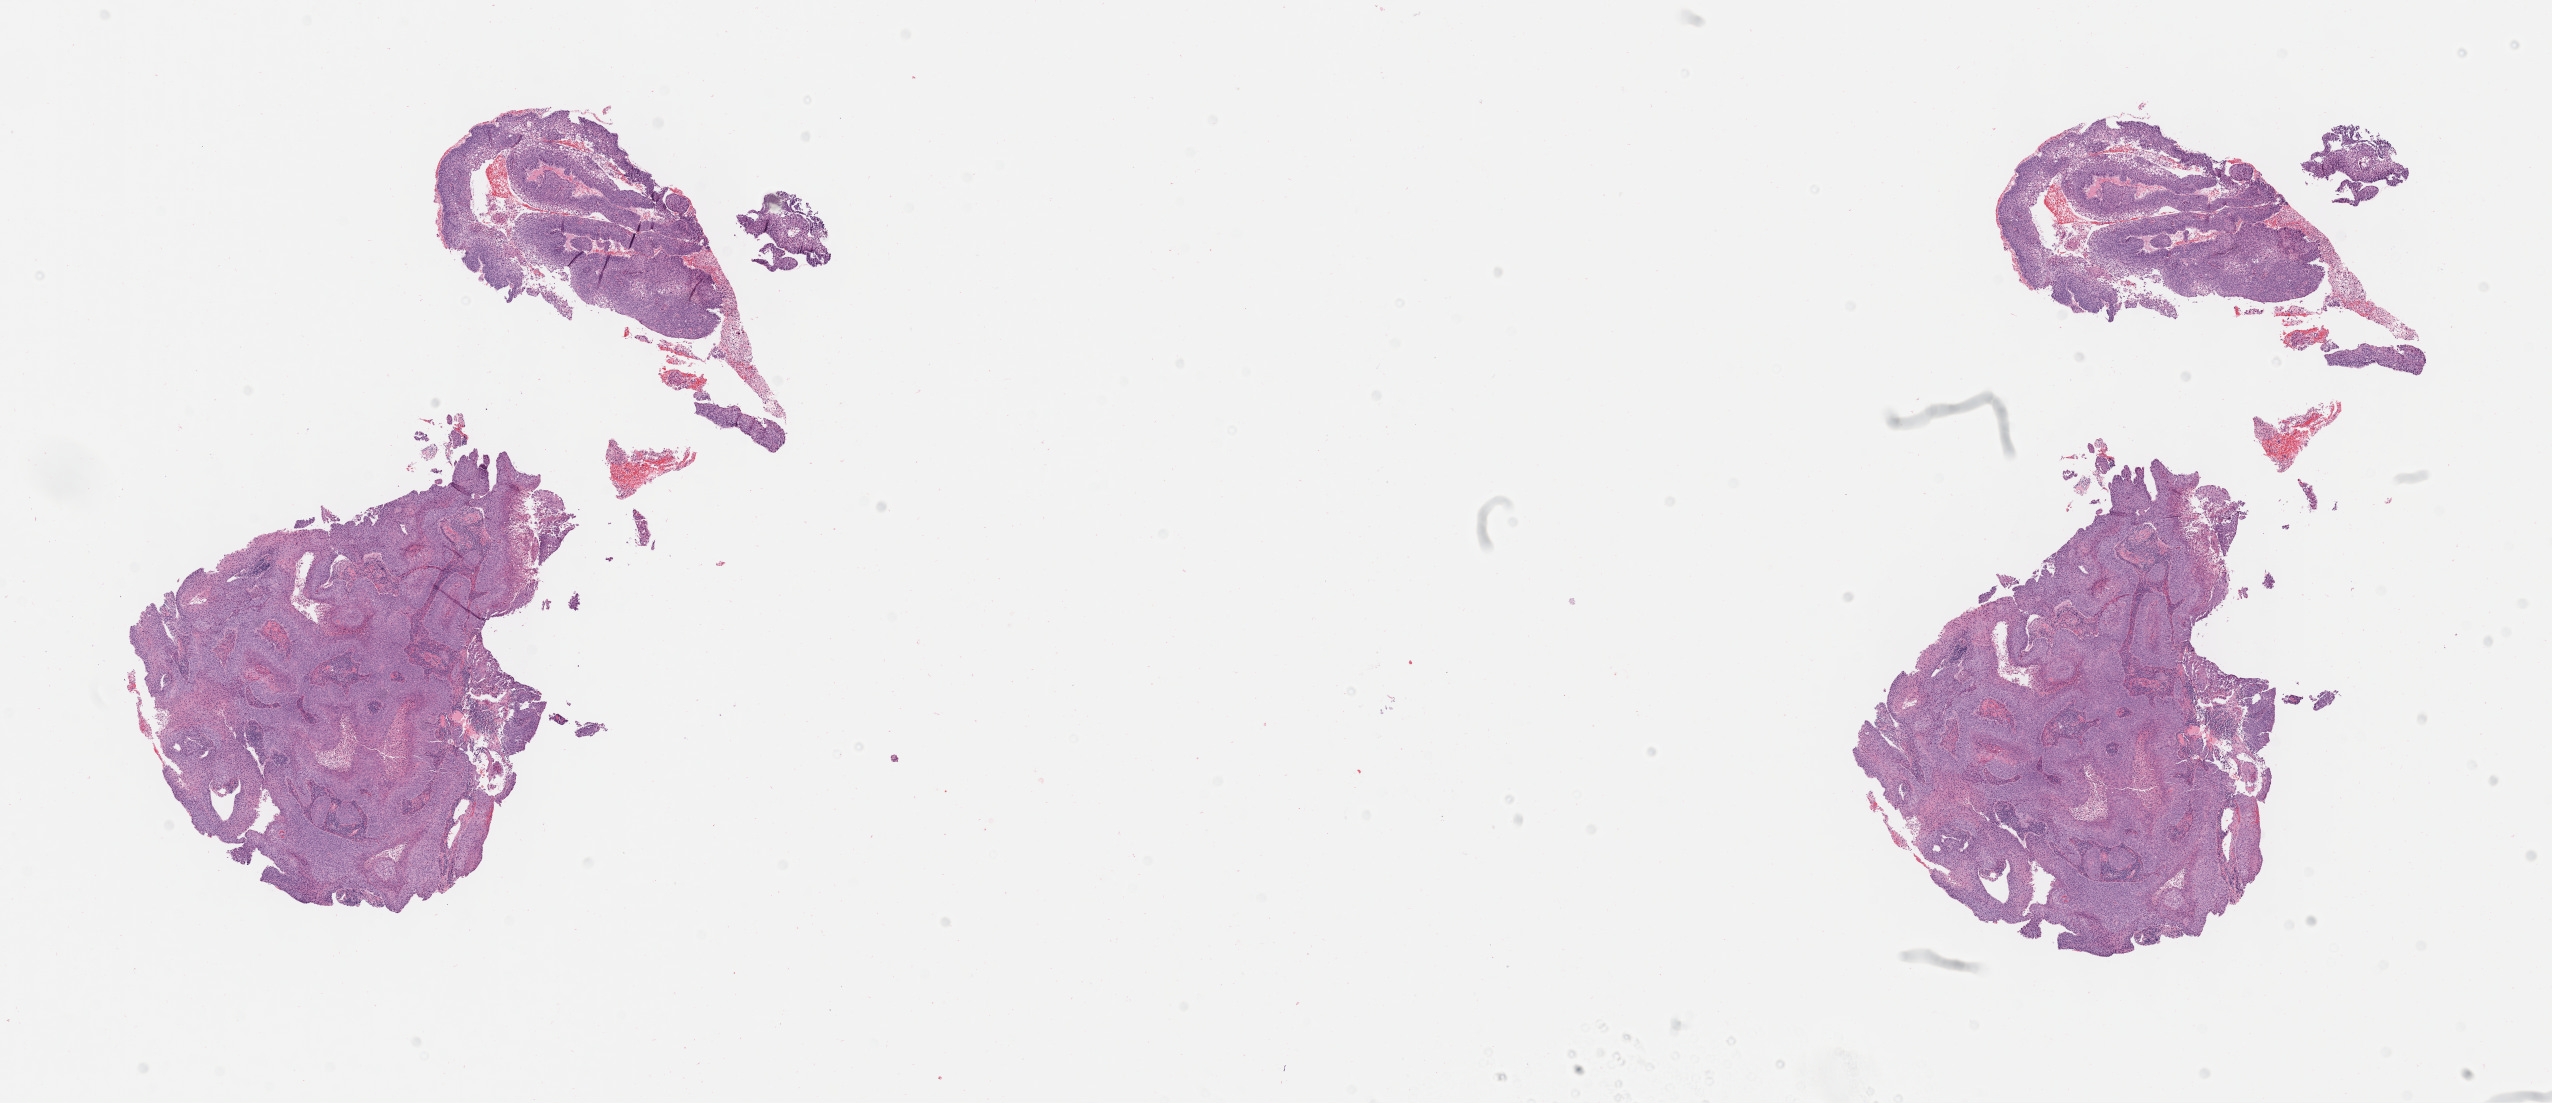
Hematoxylin and eosin (H&E) whole-slide image — a low-resolution overview of the entire scanned area, about 20.6 x 8.9 mm. Tumor tissue. Site: cervix. Female patient, 54 years old.
Histologic diagnosis: Squamous cell carcinoma, large cell, nonkeratinizing, NOS.